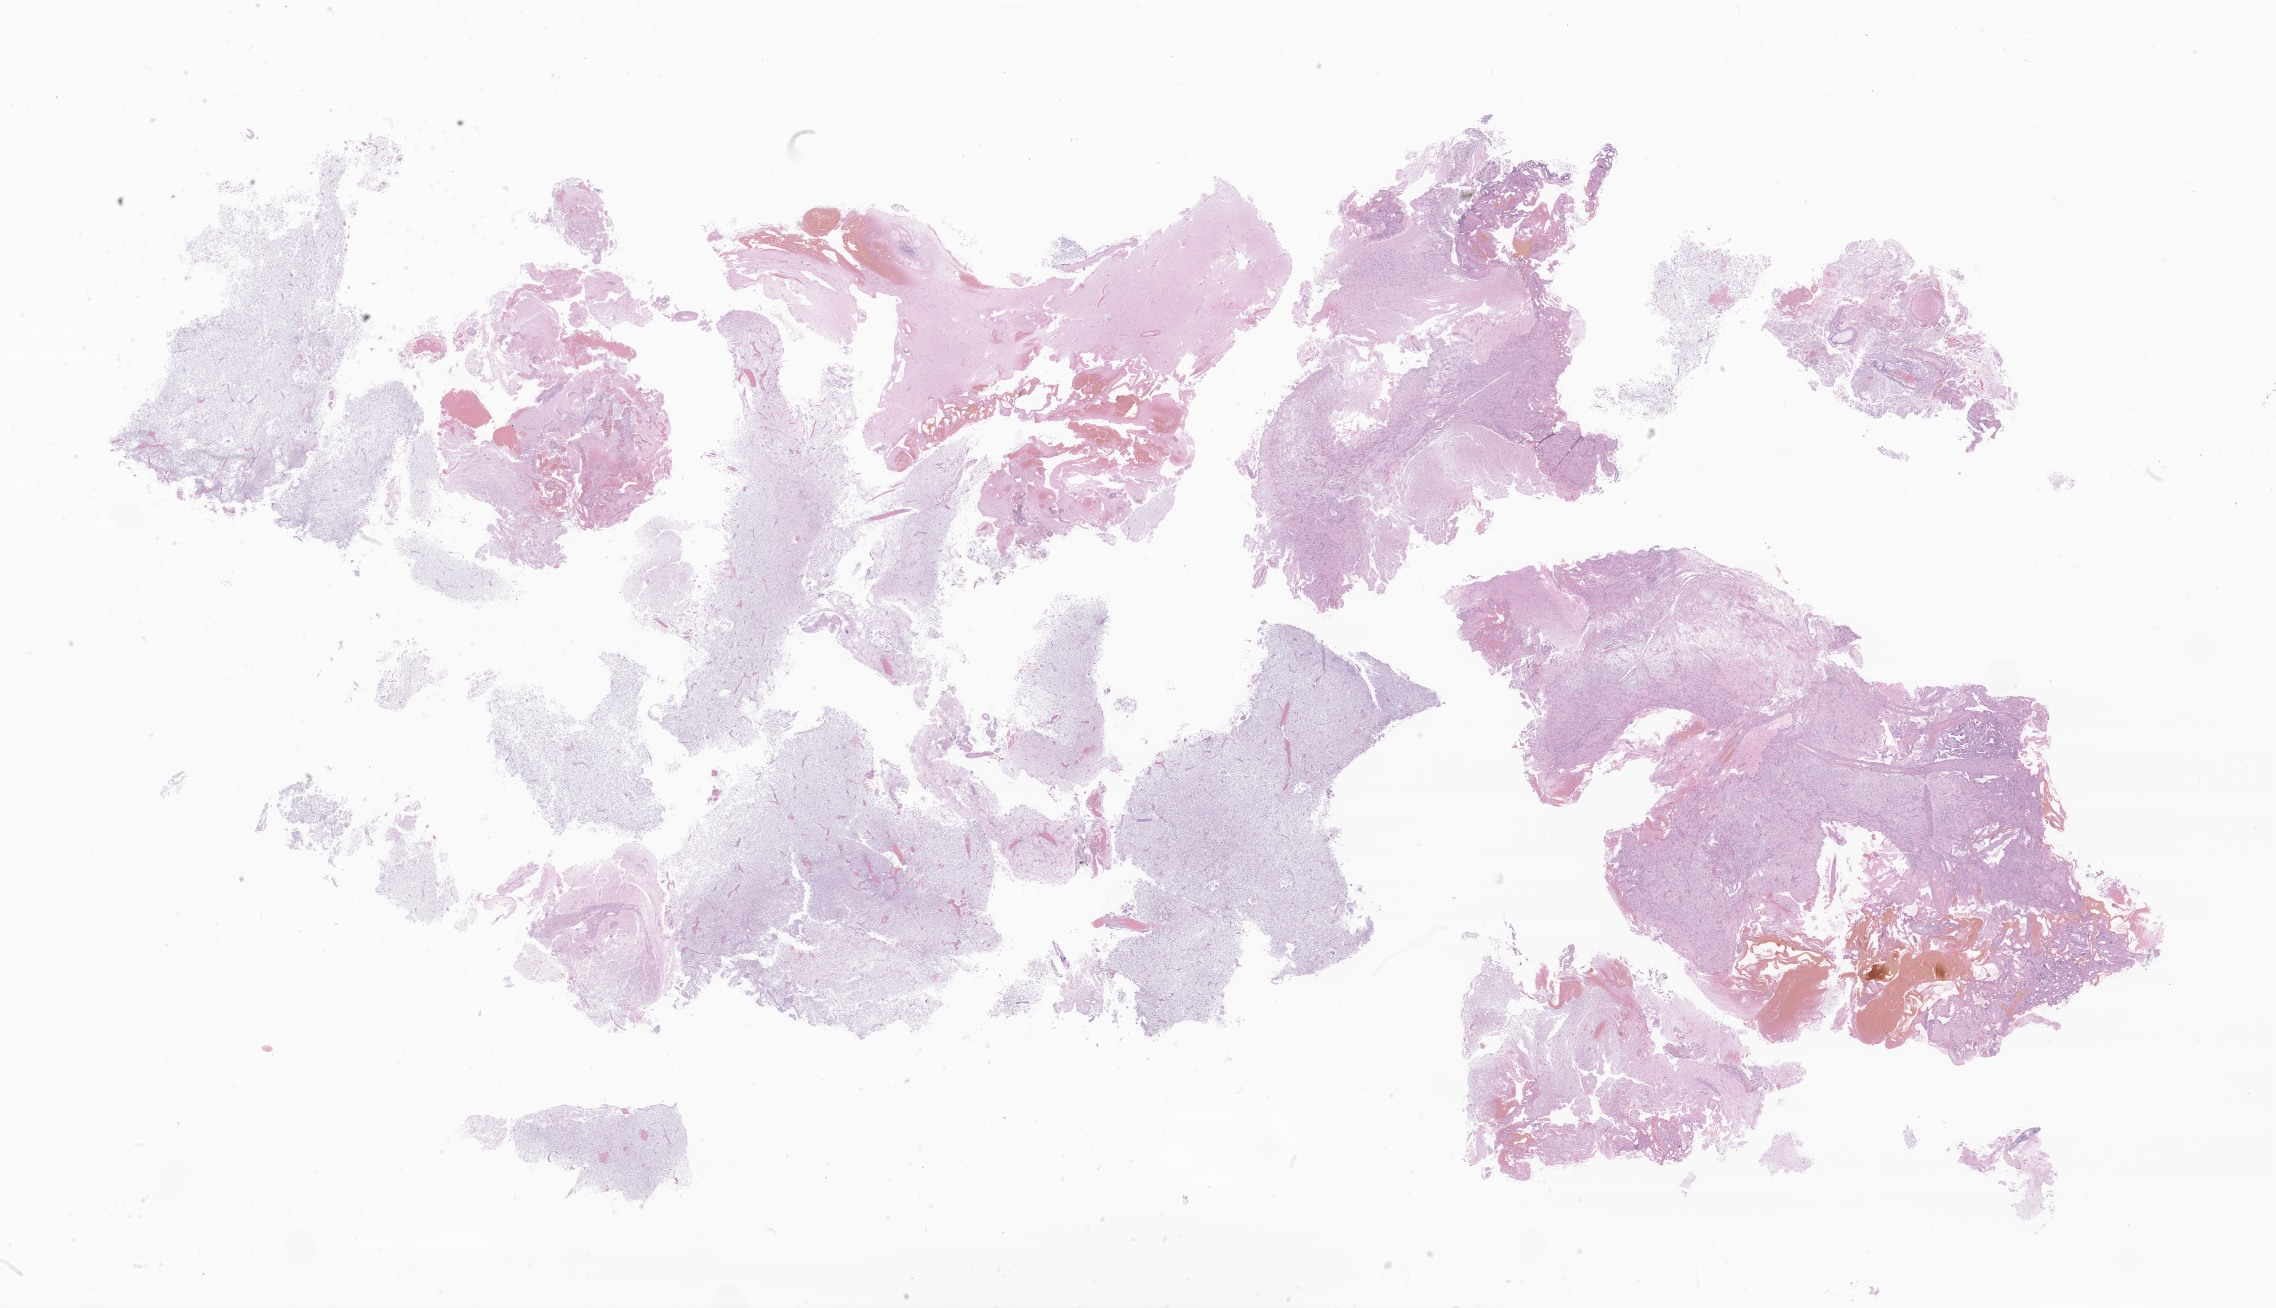
H&E whole-slide image of tumor tissue from the brain, low-resolution overview of the scanned area, about 38.4 x 22.1 mm; formalin-fixed, paraffin-embedded (FFPE) tissue. Patient female; age 49 months (4 years 1 month).
Diagnosis: Medulloblastoma, NOS.